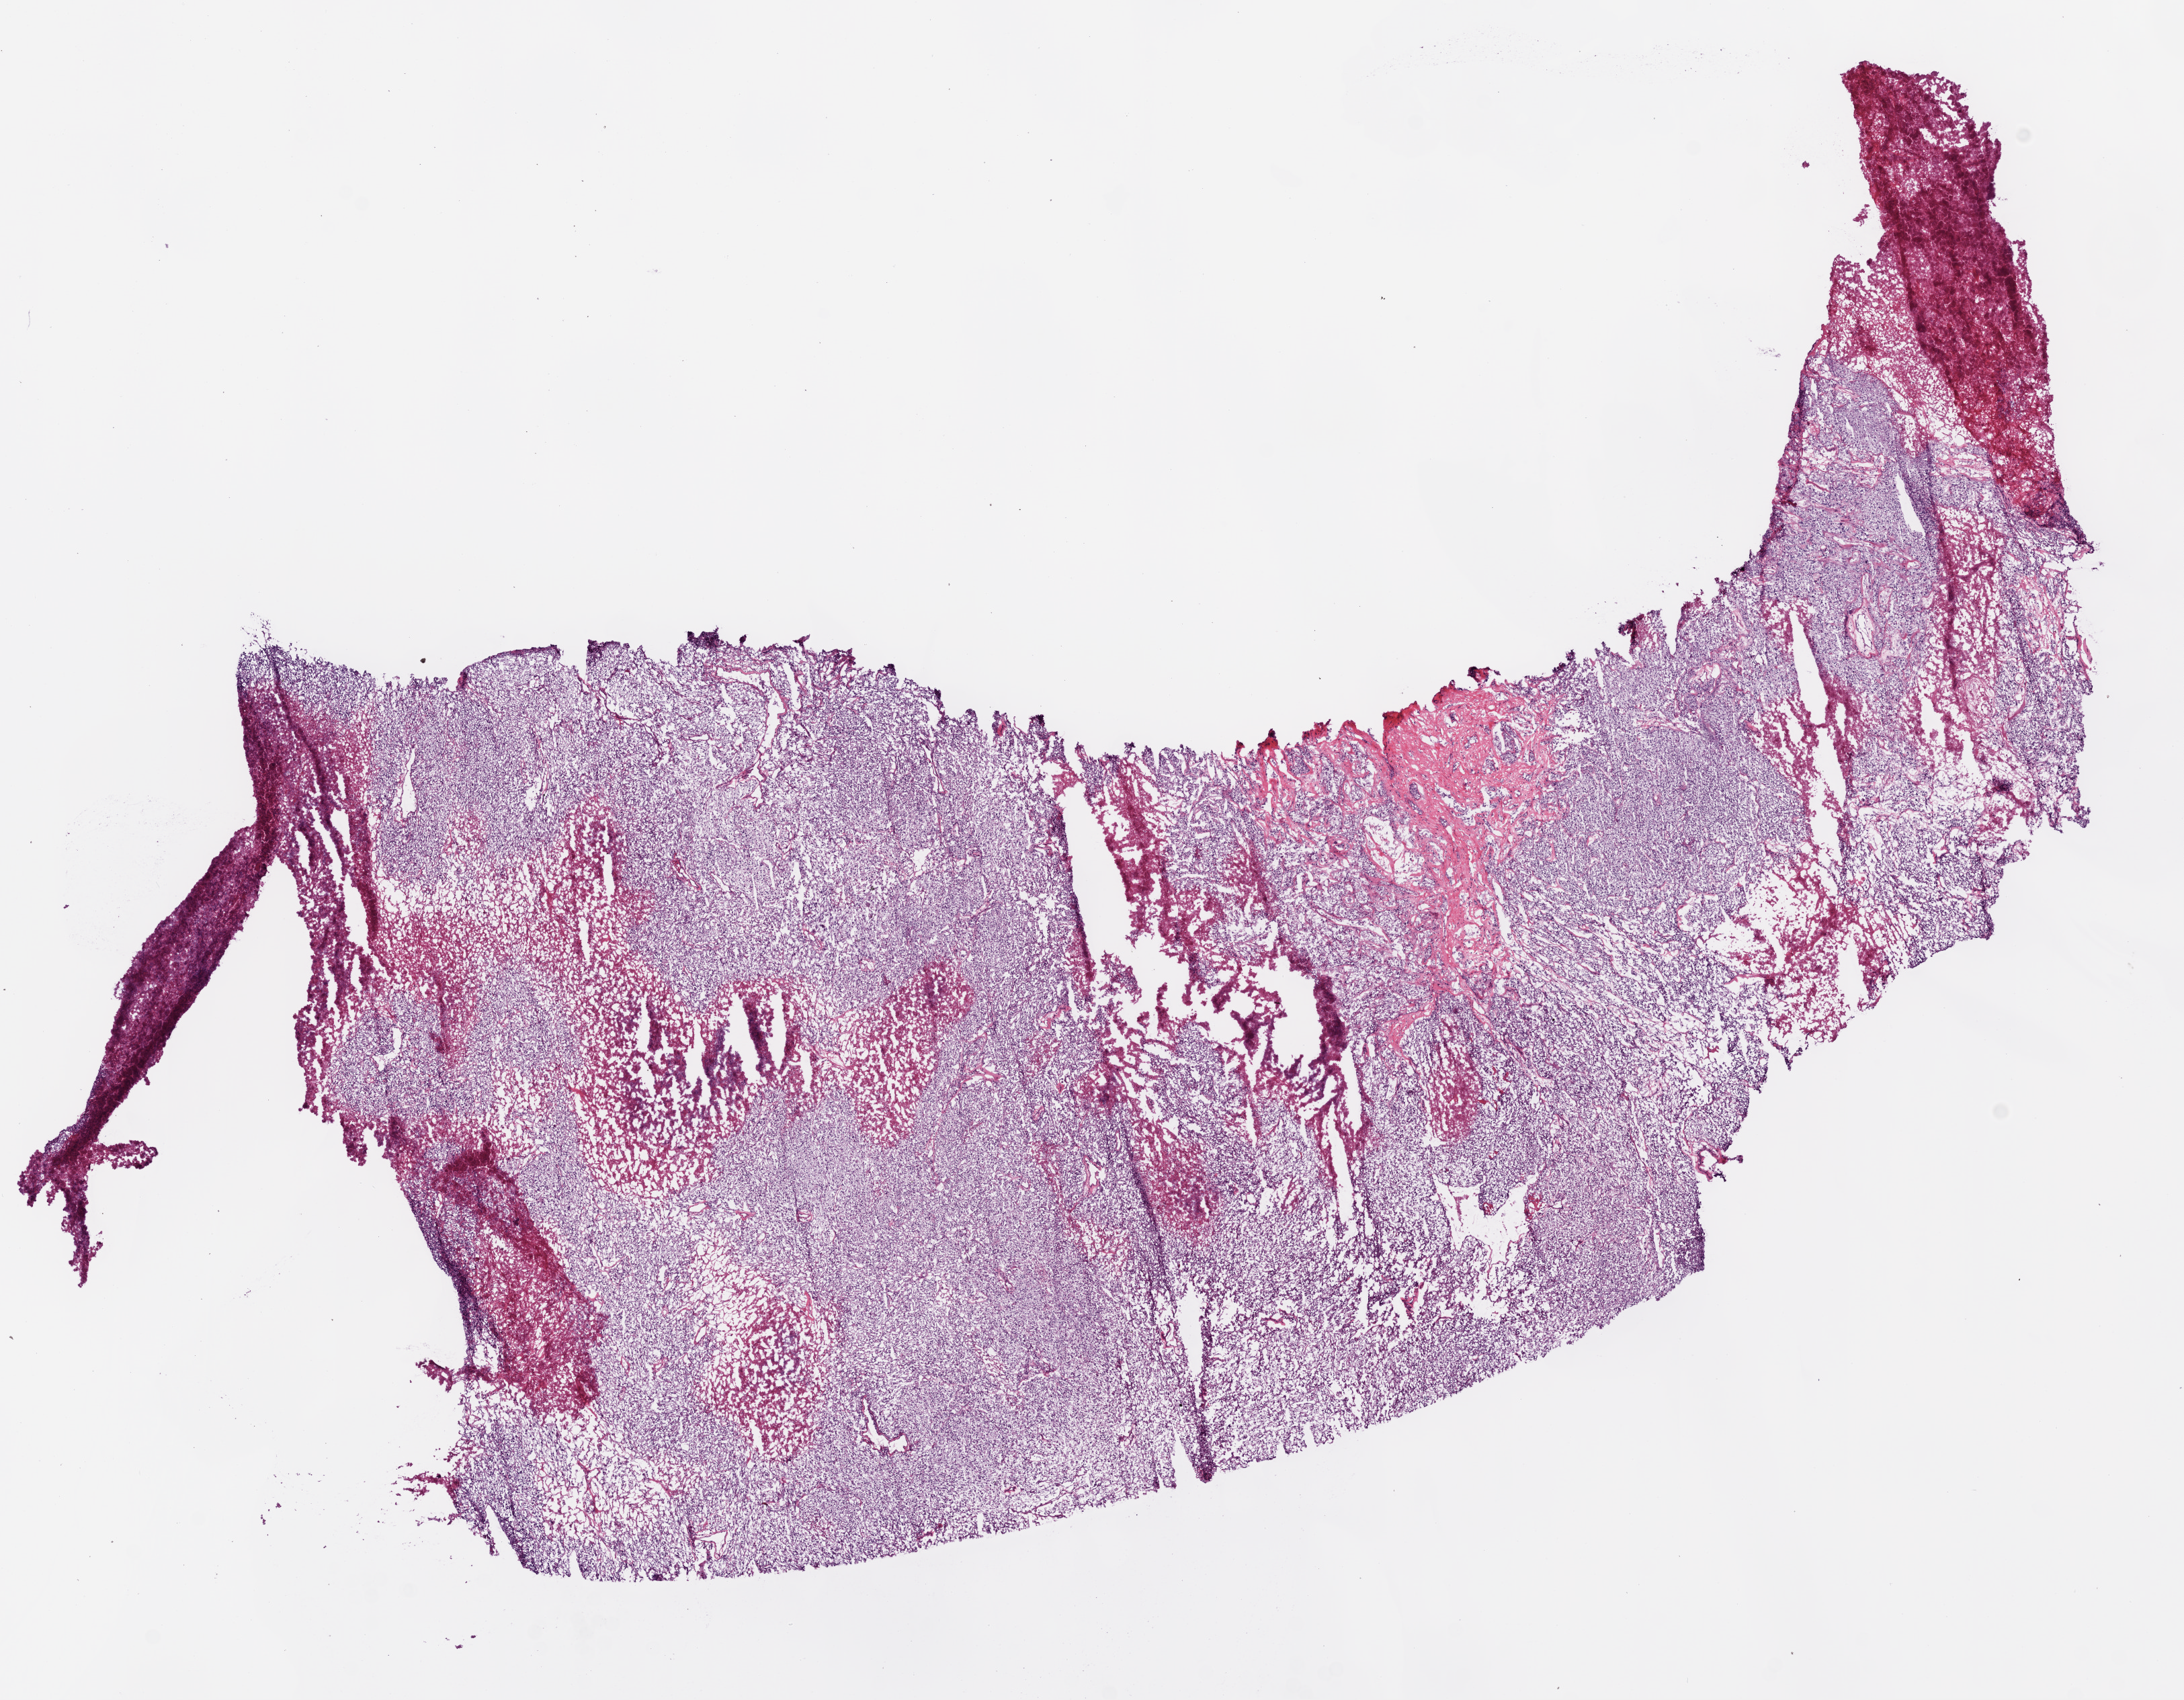
Whole-slide histology image, Hematoxylin and eosin (H&E) stained — low-resolution overview of the scanned area, about 13.0 x 10.2 mm. Frozen section from the top of the tissue portion. Kidney, primary tumour sample. Male patient; age at initial diagnosis 68 years. Histologic grade: G3 (poorly differentiated). Slide review estimates, as recorded: tumour cells 77%, tumour nuclei 80%, normal cells 0%, stromal cells 5%, necrosis 18%. Infiltration values recorded for this section: lymphocyte infiltration 15%, monocyte infiltration 1%, neutrophil infiltration 0%.
Diagnosis: Clear cell adenocarcinoma, NOS. AJCC pathologic stage: I.